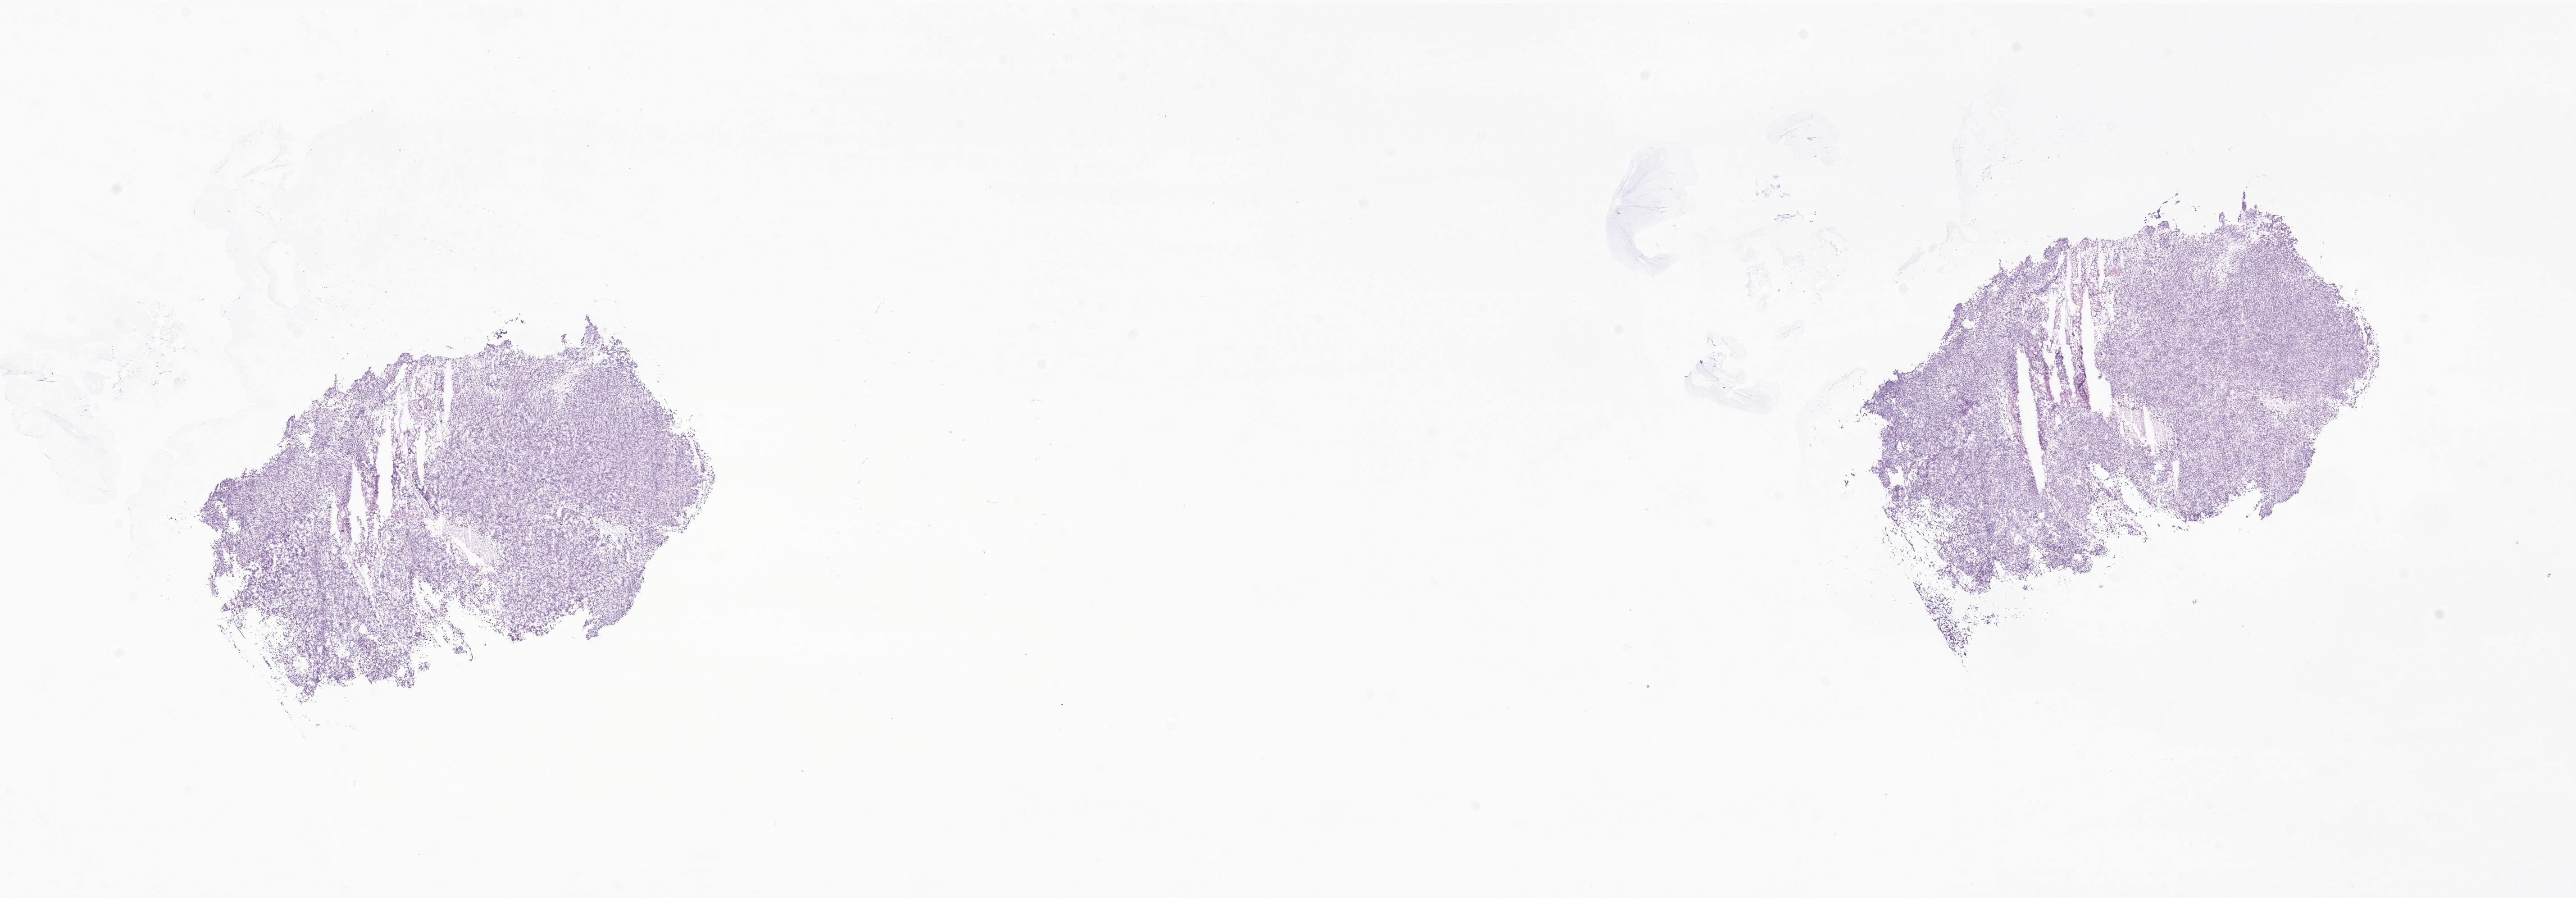
Whole-slide image, haematoxylin and eosin stain of tumor tissue from the frontal lobe, shown as a low-resolution overview of the whole scanned area (about 24.1 x 8.4 mm), cryosection (OCT / tissue freezing medium). Patient male; age 53 months.
• diagnosis: CNS embryonal tumor, NOS